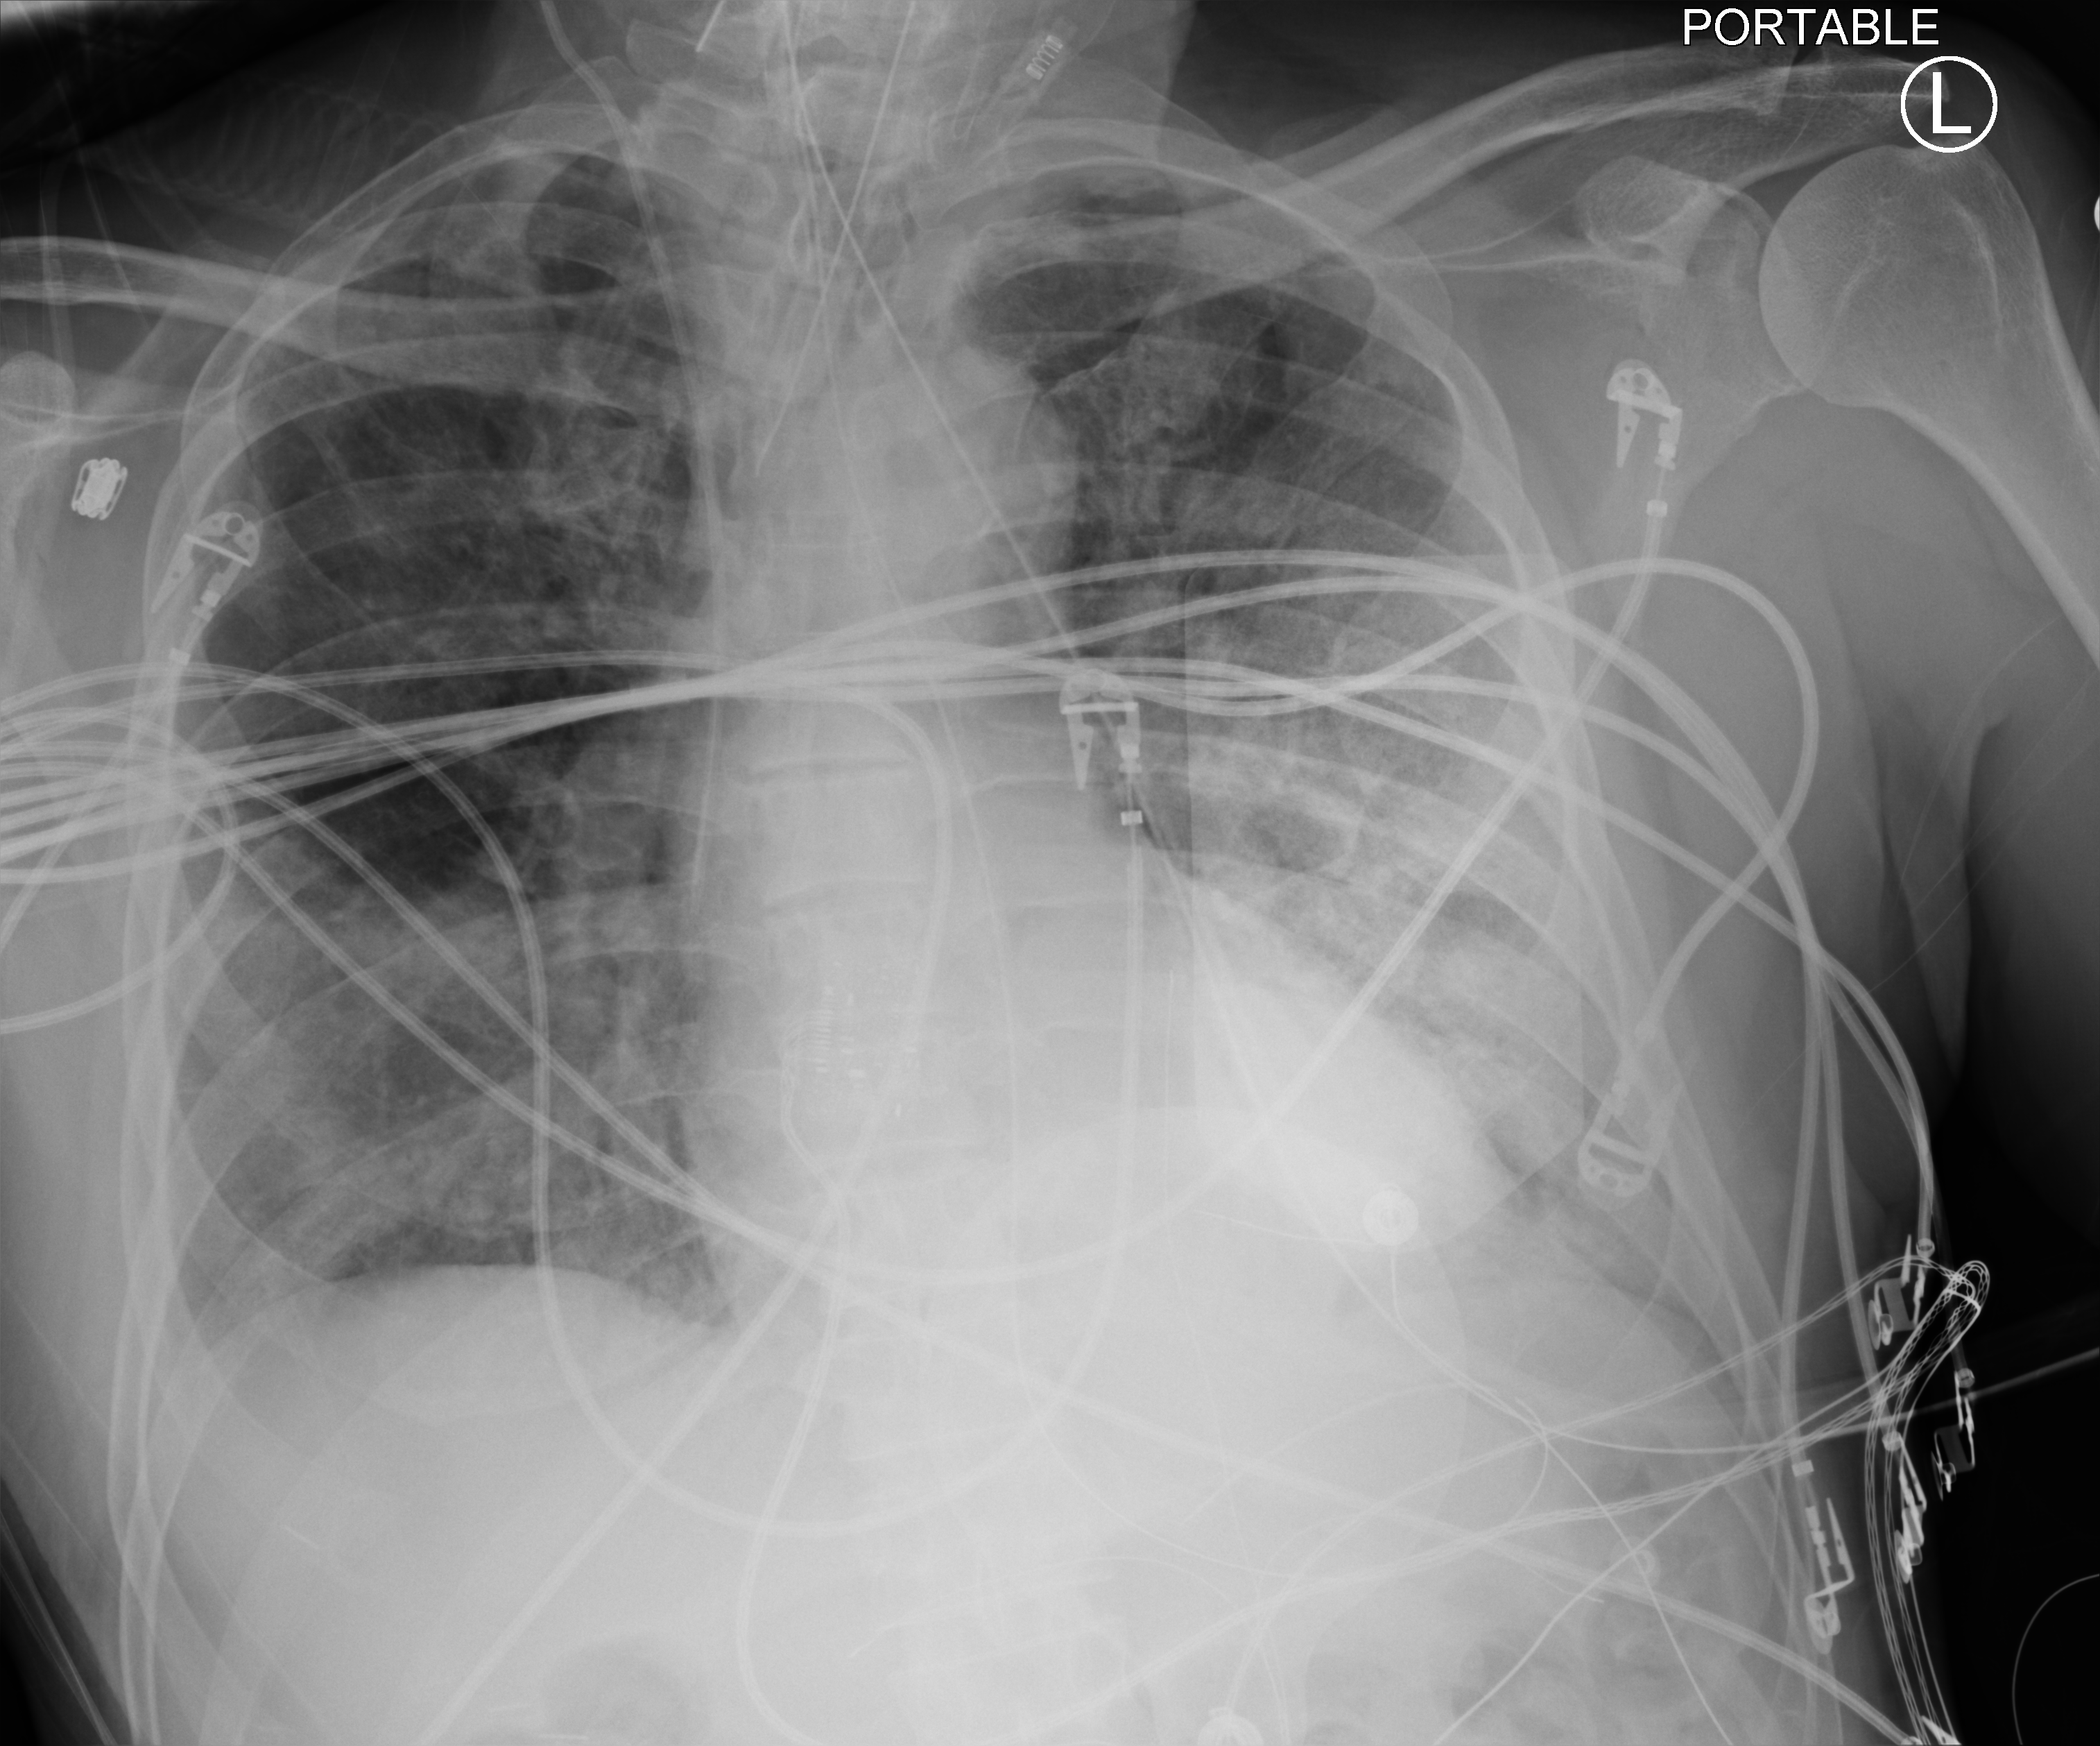
Portable chest radiograph. Patient hospitalised with COVID-19; male, aged 60–74 years.
Hospital-stay facts (about this admission, not read from this image; timing relative to this image not recorded):
- admitted to intensive care during this hospital stay: yes
- hypertension (admission record): no
- mechanically ventilated during this hospital stay: yes